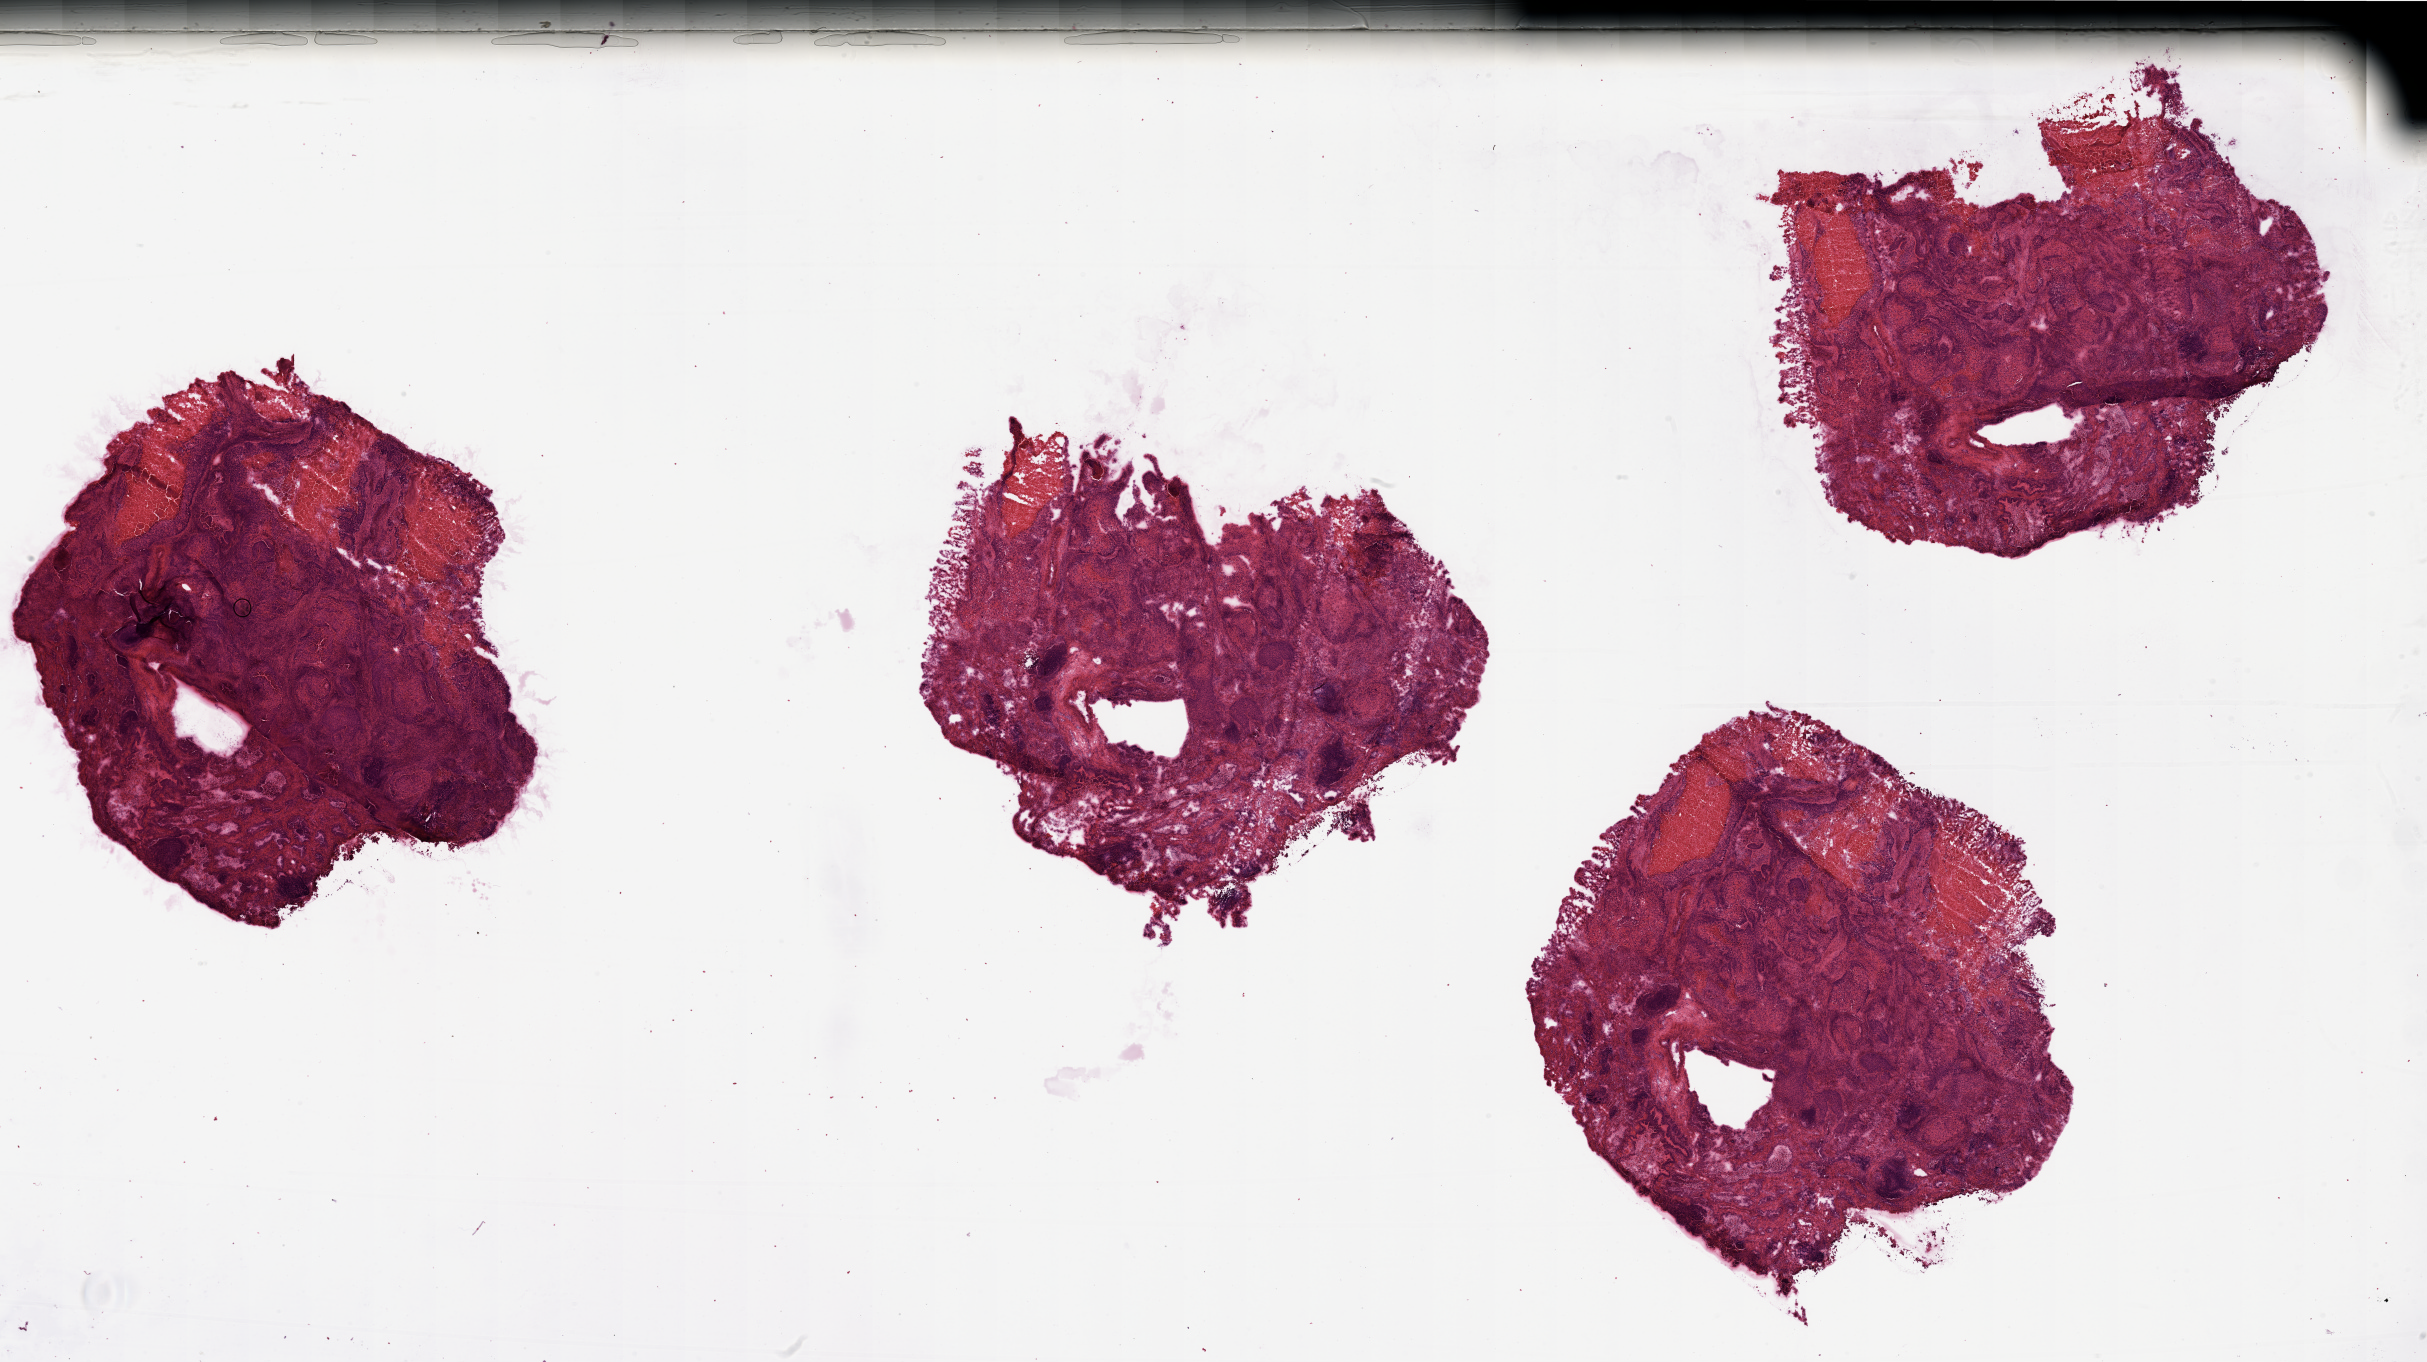
Whole-slide histology image, H&E — shown as a low-resolution overview of the whole scanned area (about 38.4 x 21.5 mm). Lung, tumour tissue. Patient: male, age 65 years.
Patient diagnosis (cohort enrolment): squamous cell carcinoma (lung). Primary tumour site (as recorded): left lower lobe.